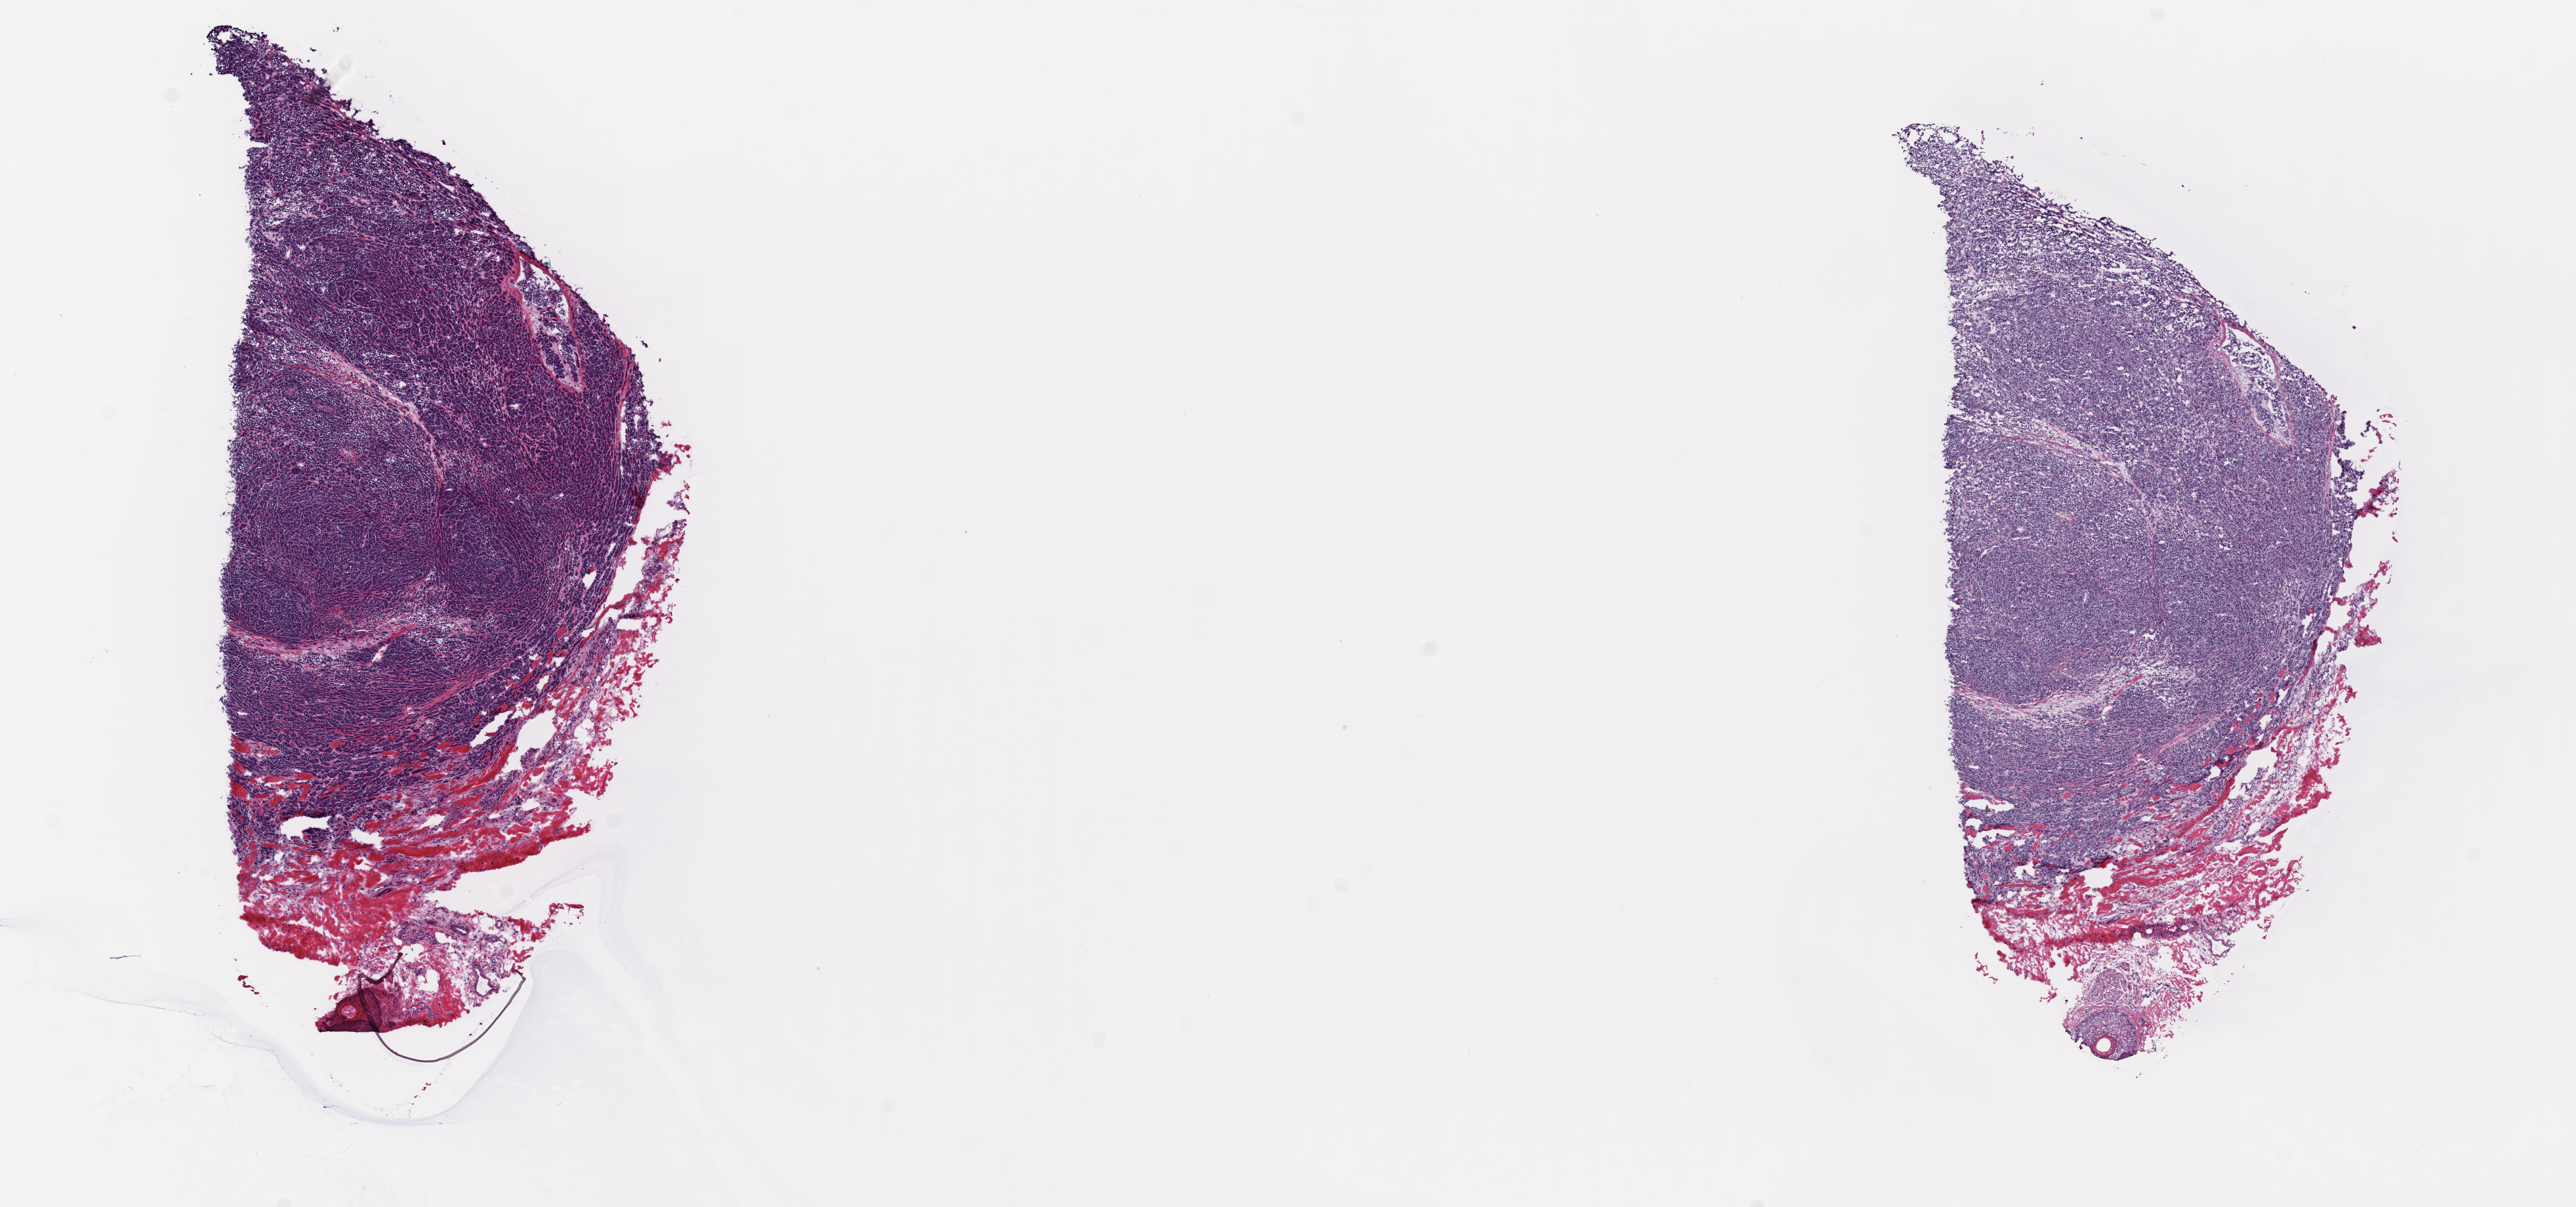
Hematoxylin and eosin (H&E) stained whole-slide image, low-resolution overview of the scanned area, about 15.5 x 7.3 mm (slide scanned at 40x). Frozen section. Metastatic tumour sample, sampled site not recorded. Patient: male, age at initial diagnosis 40 years. Composition of this section per pathologist review: tumour cells 87%, tumour nuclei 95%, normal cells 0%, stromal cells 12%, necrosis 1%. Inflammatory infiltration, as recorded: lymphocyte infiltration 1%, monocyte infiltration 1%, neutrophil infiltration 0%.
This section: metastatic tumour tissue. Patient diagnosis: Malignant melanoma, NOS.